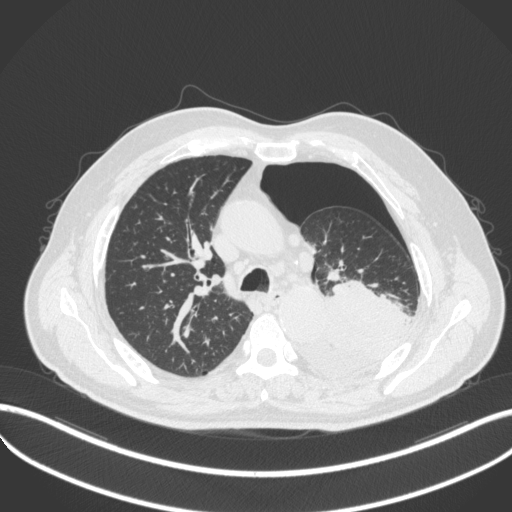
Chest CT, one axial slice. Position 352 of 466 along the scan axis. Lung window (W 1500 / L -600 HU). 1 mm slice thickness. 512 × 512 image matrix, field of view 400 × 400 mm. Male patient, age 76 years. Case-level facts recorded for this patient, not image findings: clinical TNM (as recorded): T3 N0 M1b.
Annotated regions visible in this slice (bounding box drawn by a radiologist):
- lung tumour (recorded histology: adenocarcinoma): bounding box <287,278,419,382> (left, top, right, bottom; pixels)